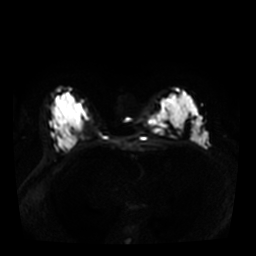
Breast MRI, one axial slice. Position 22 of 36 along the scan axis. Diffusion-weighted series; image 2 of 4 stored at this slice position (different b-values; order by instance number). 3 T. 5 mm slice thickness. 256 × 256 image matrix, field of view 340 × 340 mm. Female patient.
Structures marked on this image (outlined manually by an expert reader):
- tumour on diffusion-weighted imaging: bounding box (x1, y1, x2, y2) in pixels: (149, 114, 165, 132)